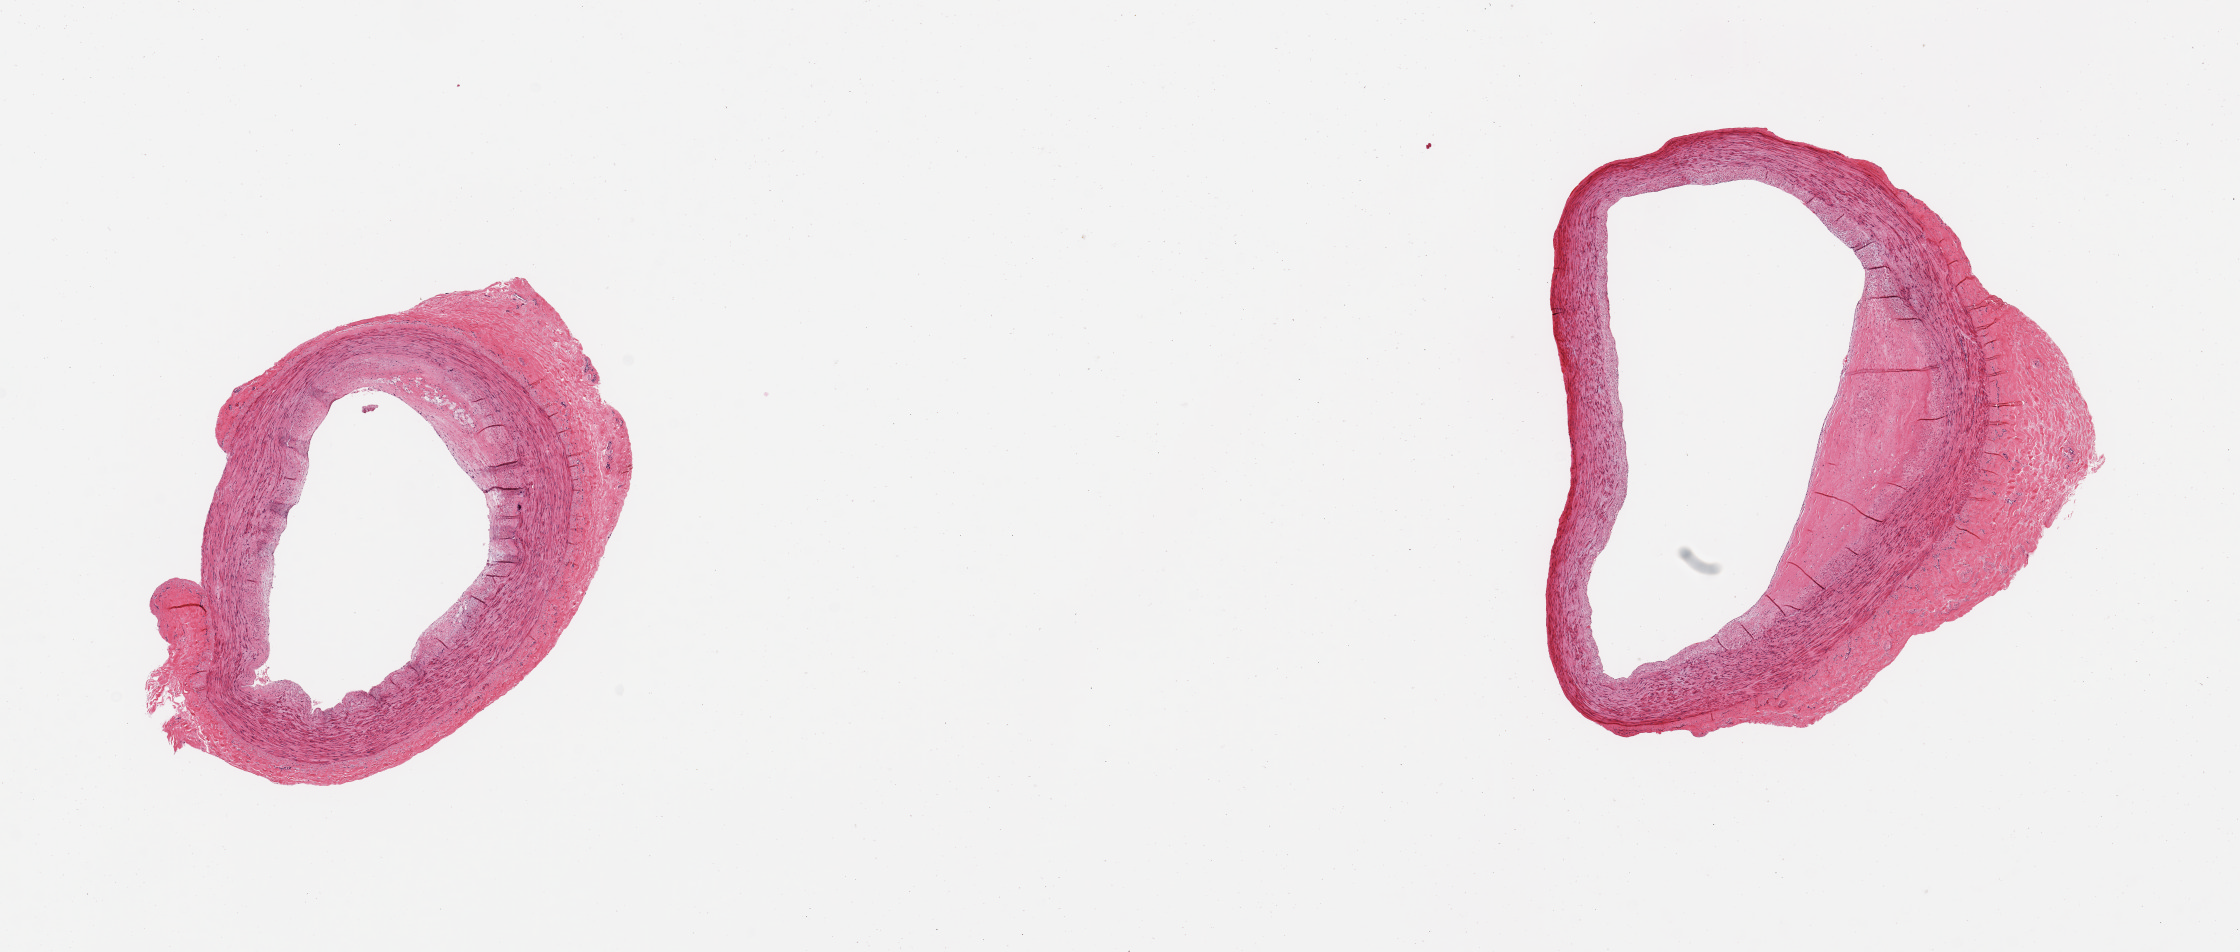
Digitized hematoxylin and eosin (H&E)-stained section, brightfield, low-resolution overview of the scanned area, about 17.7 x 7.5 mm, PAXgene-fixed paraffin-embedded (PFPE) section, sampled site (target tissue): tibial artery, donor tissue sample. Donor sex: male.
Reviewer comment on this tissue sample: 2 pieces; mild to focally moderate degree of intimal fibroatheromatous plaques; widely patent lumens; minute calcification.